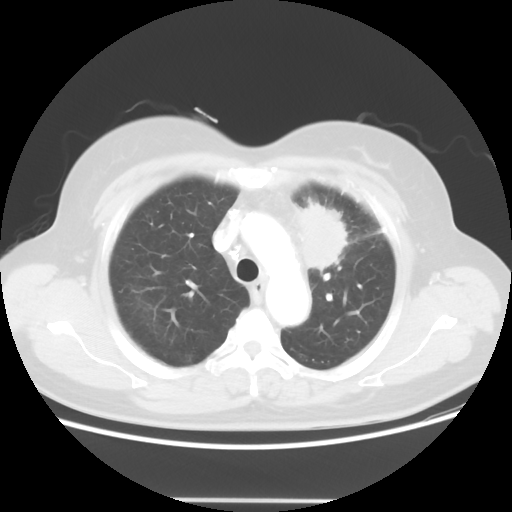
Chest CT, one axial slice; position 41 of 52 along the scan axis; lung window (W 1500 / L -600 HU); 512 × 512 image matrix, field of view 382 × 382 mm. Patient: female, 52 years. Case-level facts recorded for this patient, not image findings: clinical TNM (as recorded): T2 N3 M0.
Annotated regions visible in this slice (rectangle marked by the reading radiologist):
- lung tumour (recorded histology: adenocarcinoma): bounding box [x1, y1, x2, y2] px = [287, 197, 351, 273]